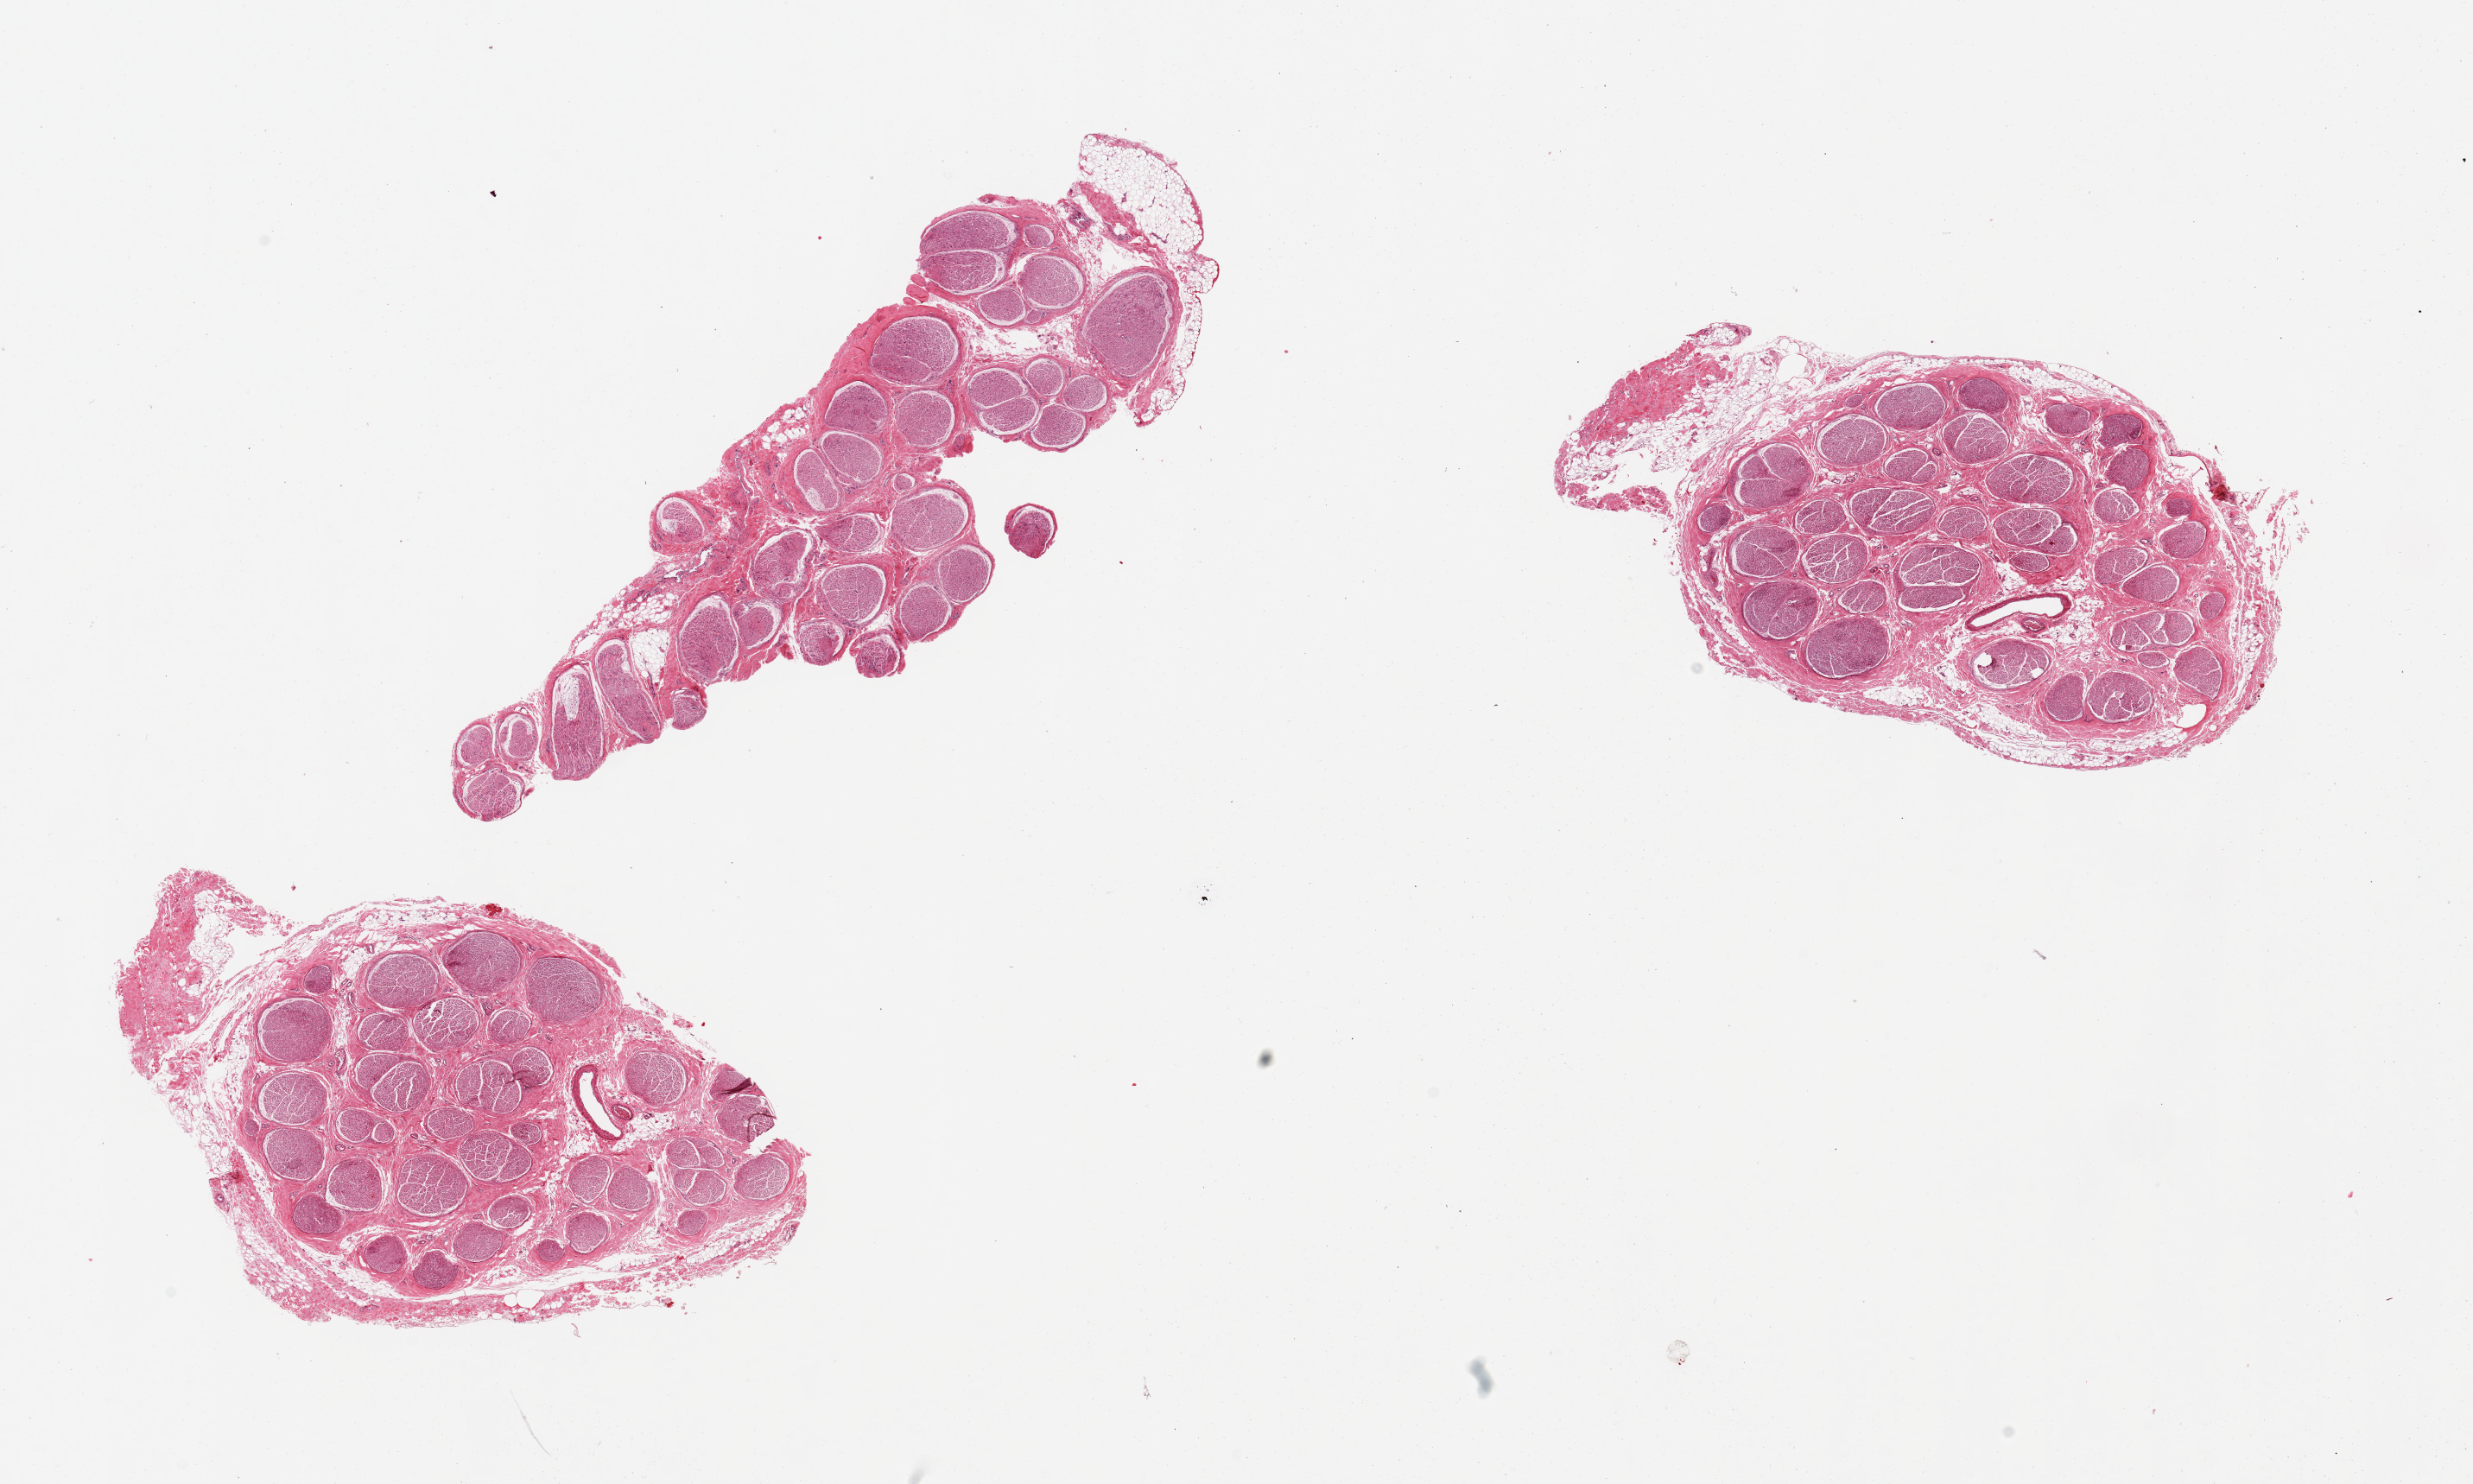
Digitized H&E-stained section — whole scanned area (about 22.6 x 13.6 mm) shown as a low-resolution overview; PAXgene-fixed, paraffin-embedded tissue; section of tibial nerve (target tissue); donor tissue sample. Donor sex: female.
Pathologist's review note for this sample: 3 pieces, two with trace adherent fatty nubbins ~0.5-1.0mm.